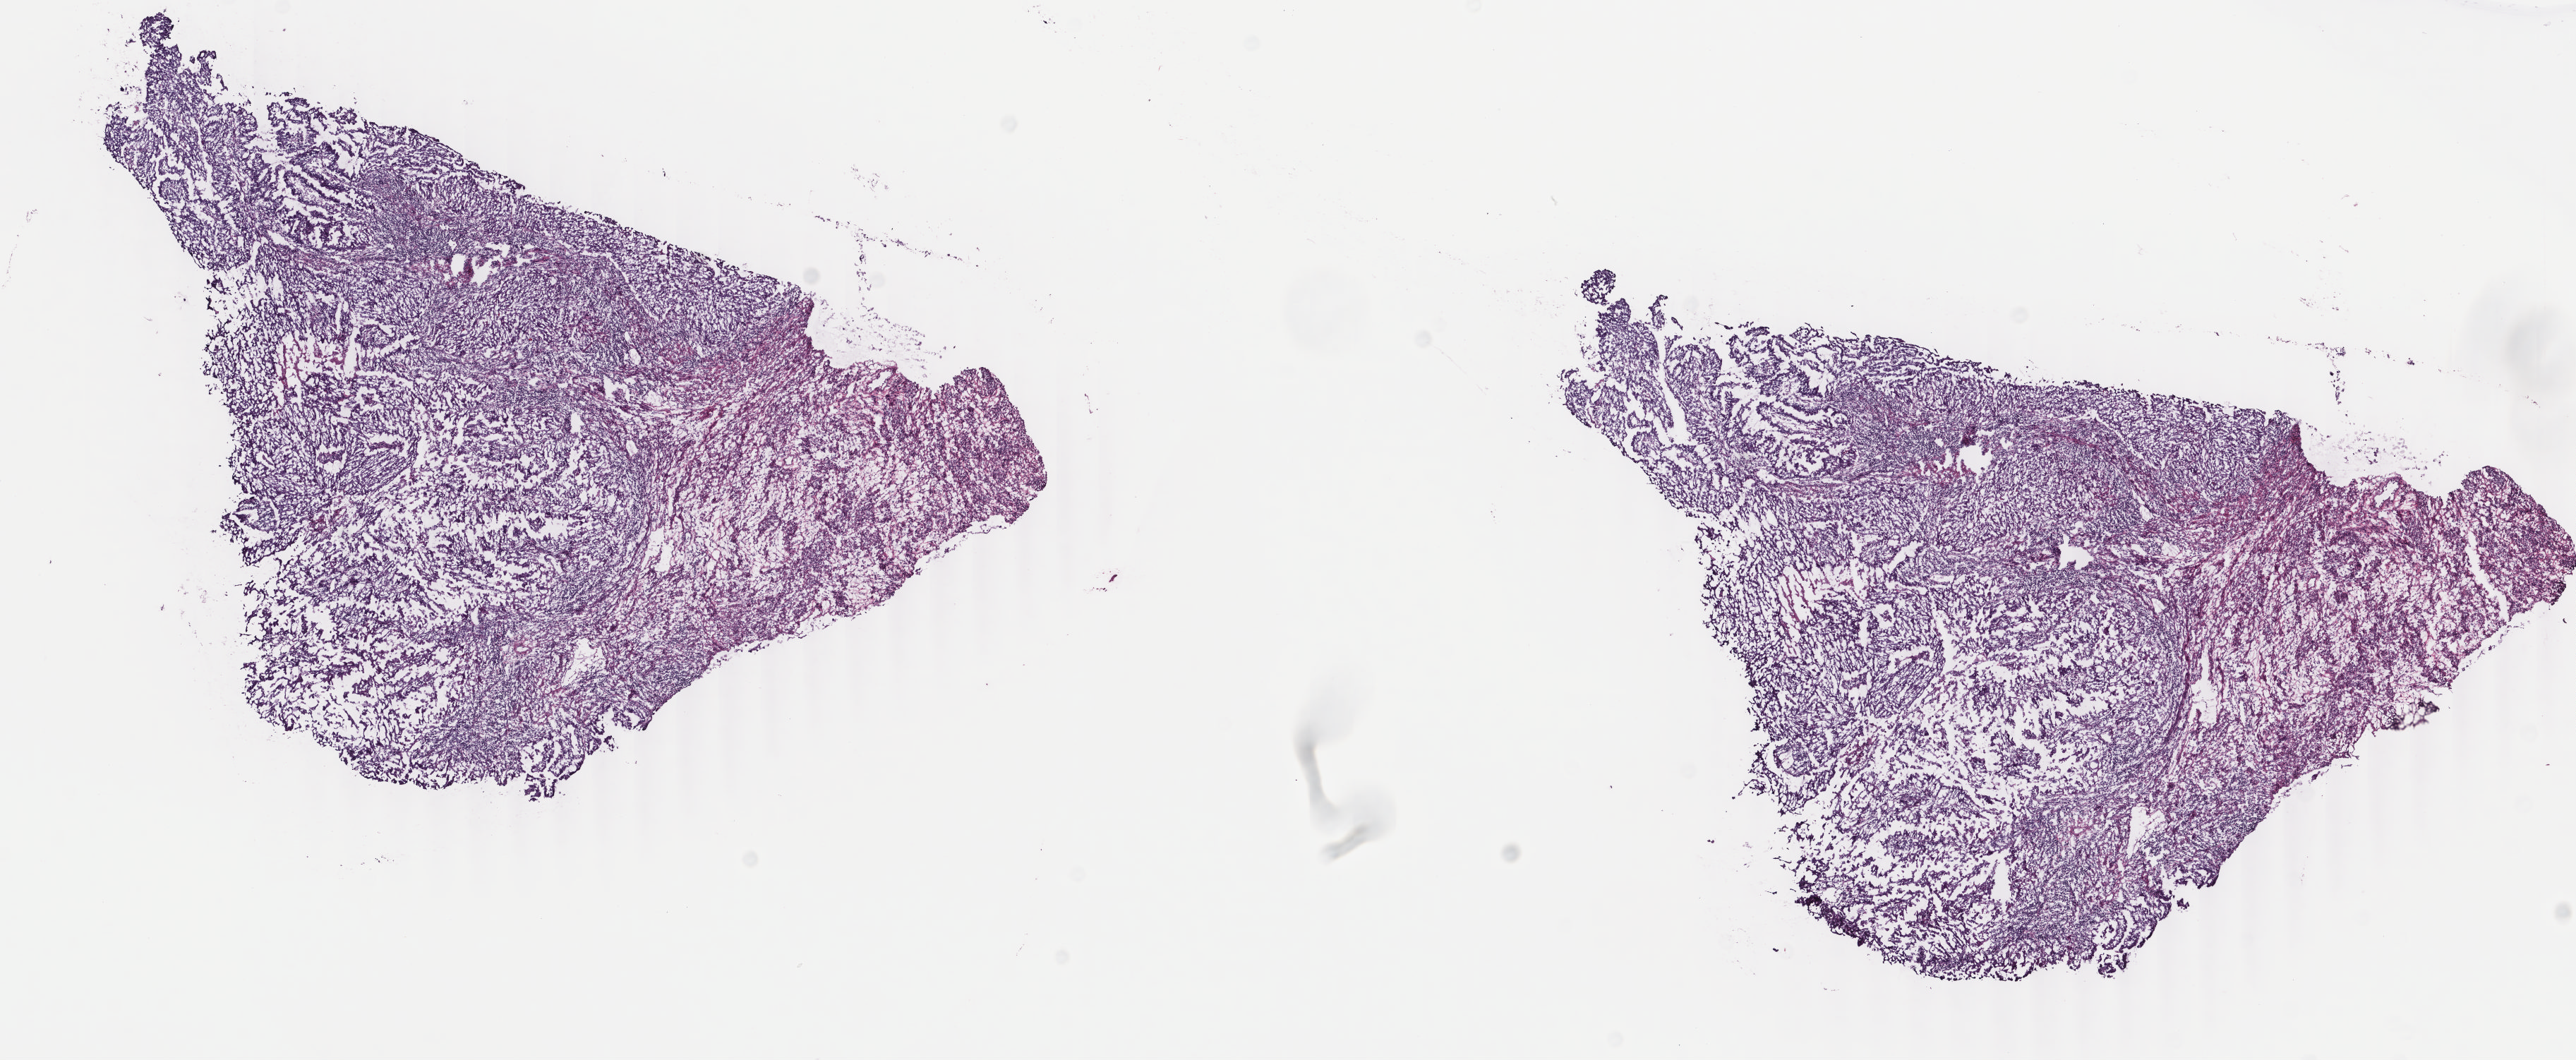
Digitized H&E-stained tissue section (whole slide), a low-resolution overview of the entire scanned area, about 14.5 x 6.0 mm; frozen section from the top of the tissue portion; primary tumour sample from the uterus. Female patient; age at initial diagnosis 83 years.
Pathologic diagnosis: Endometrioid adenocarcinoma, NOS (endometrium).